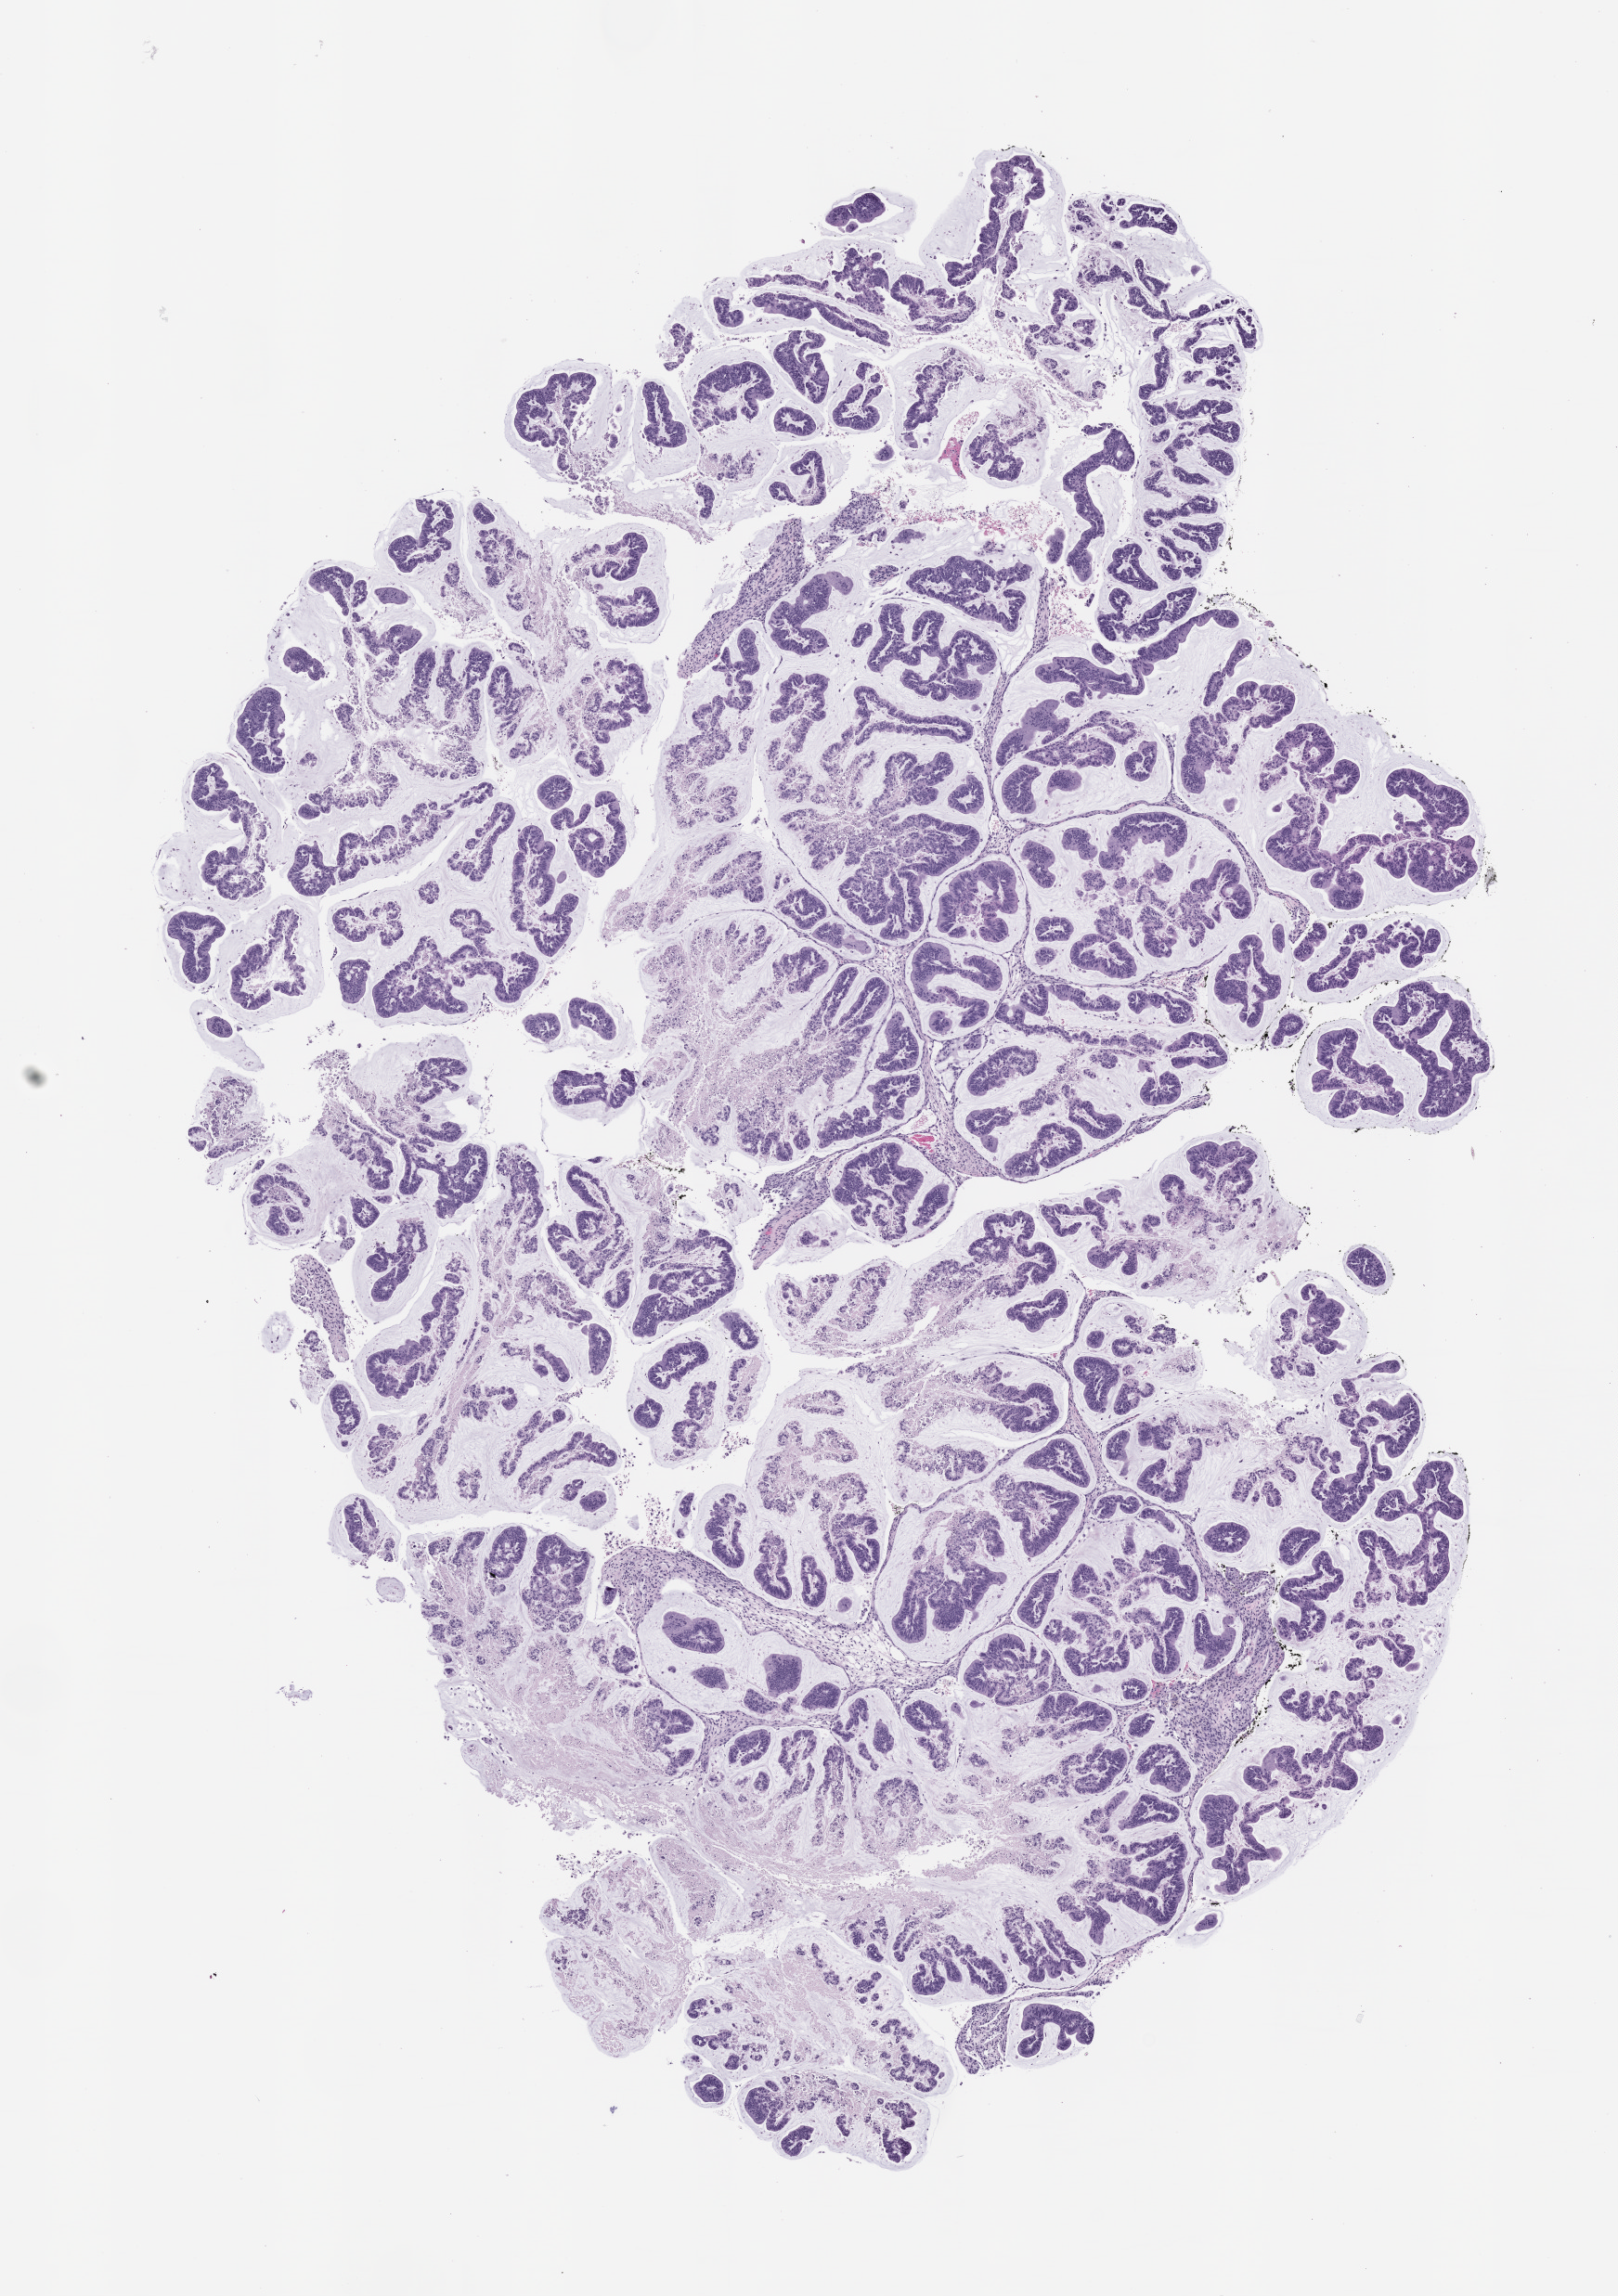
Whole-slide image, hematoxylin and eosin (H&E): patient-derived xenograft (human tumor grown in a mouse), passage 1 — low-resolution overview of the scanned area, about 7.0 x 9.9 mm. Formalin-fixed, paraffin-embedded (FFPE) tissue. Tumor site category: colon.
* originating patient diagnosis: Colon Adenocarcinoma